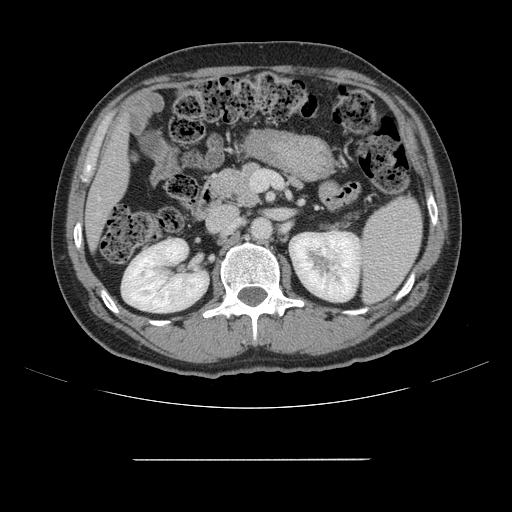
Contrast-enhanced abdominal CT, one axial slice. Slice 66 of 164 in the series (ordered by position). 120 kVp. Intravenous contrast given. Soft-tissue window (W 400 / L 40 HU). 2.5 mm slice thickness. 512 × 512 image matrix, field of view 404 × 404 mm. Male patient, age 54 years. Case-level facts recorded for this patient, not image findings: diagnosis: colorectal cancer liver metastases, imaged before liver resection; multiple liver metastases: yes; largest metastasis: 1 cm; disease in both lobes: no.
Outlined on this slice (outlined manually by an expert reader):
- liver: bounding box <86,123,127,244> (left, top, right, bottom; pixels)
- planned liver remnant (the part of the liver to remain after resection): <87,122,128,245>